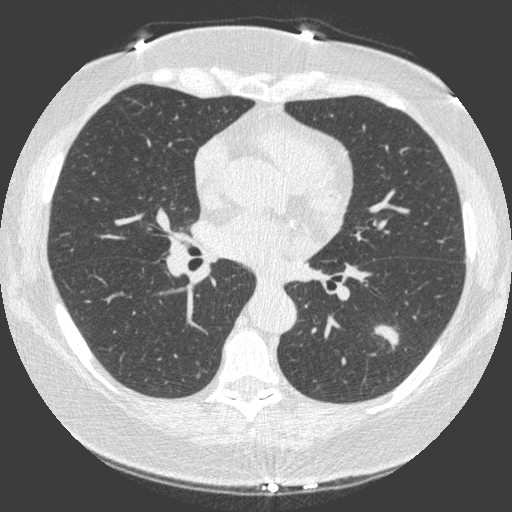
Low-dose screening chest CT, one axial slice. Position 83 of 149 along the scan axis. Lung window (W 1500 / L -600 HU). 1 mm slice thickness. 512 × 512 image matrix.
Annotated regions visible in this slice (manually delineated by an expert):
- lesion 1 (tumor, lower lobe of left lung): bounding box [x1, y1, x2, y2] px = [375, 325, 398, 349]